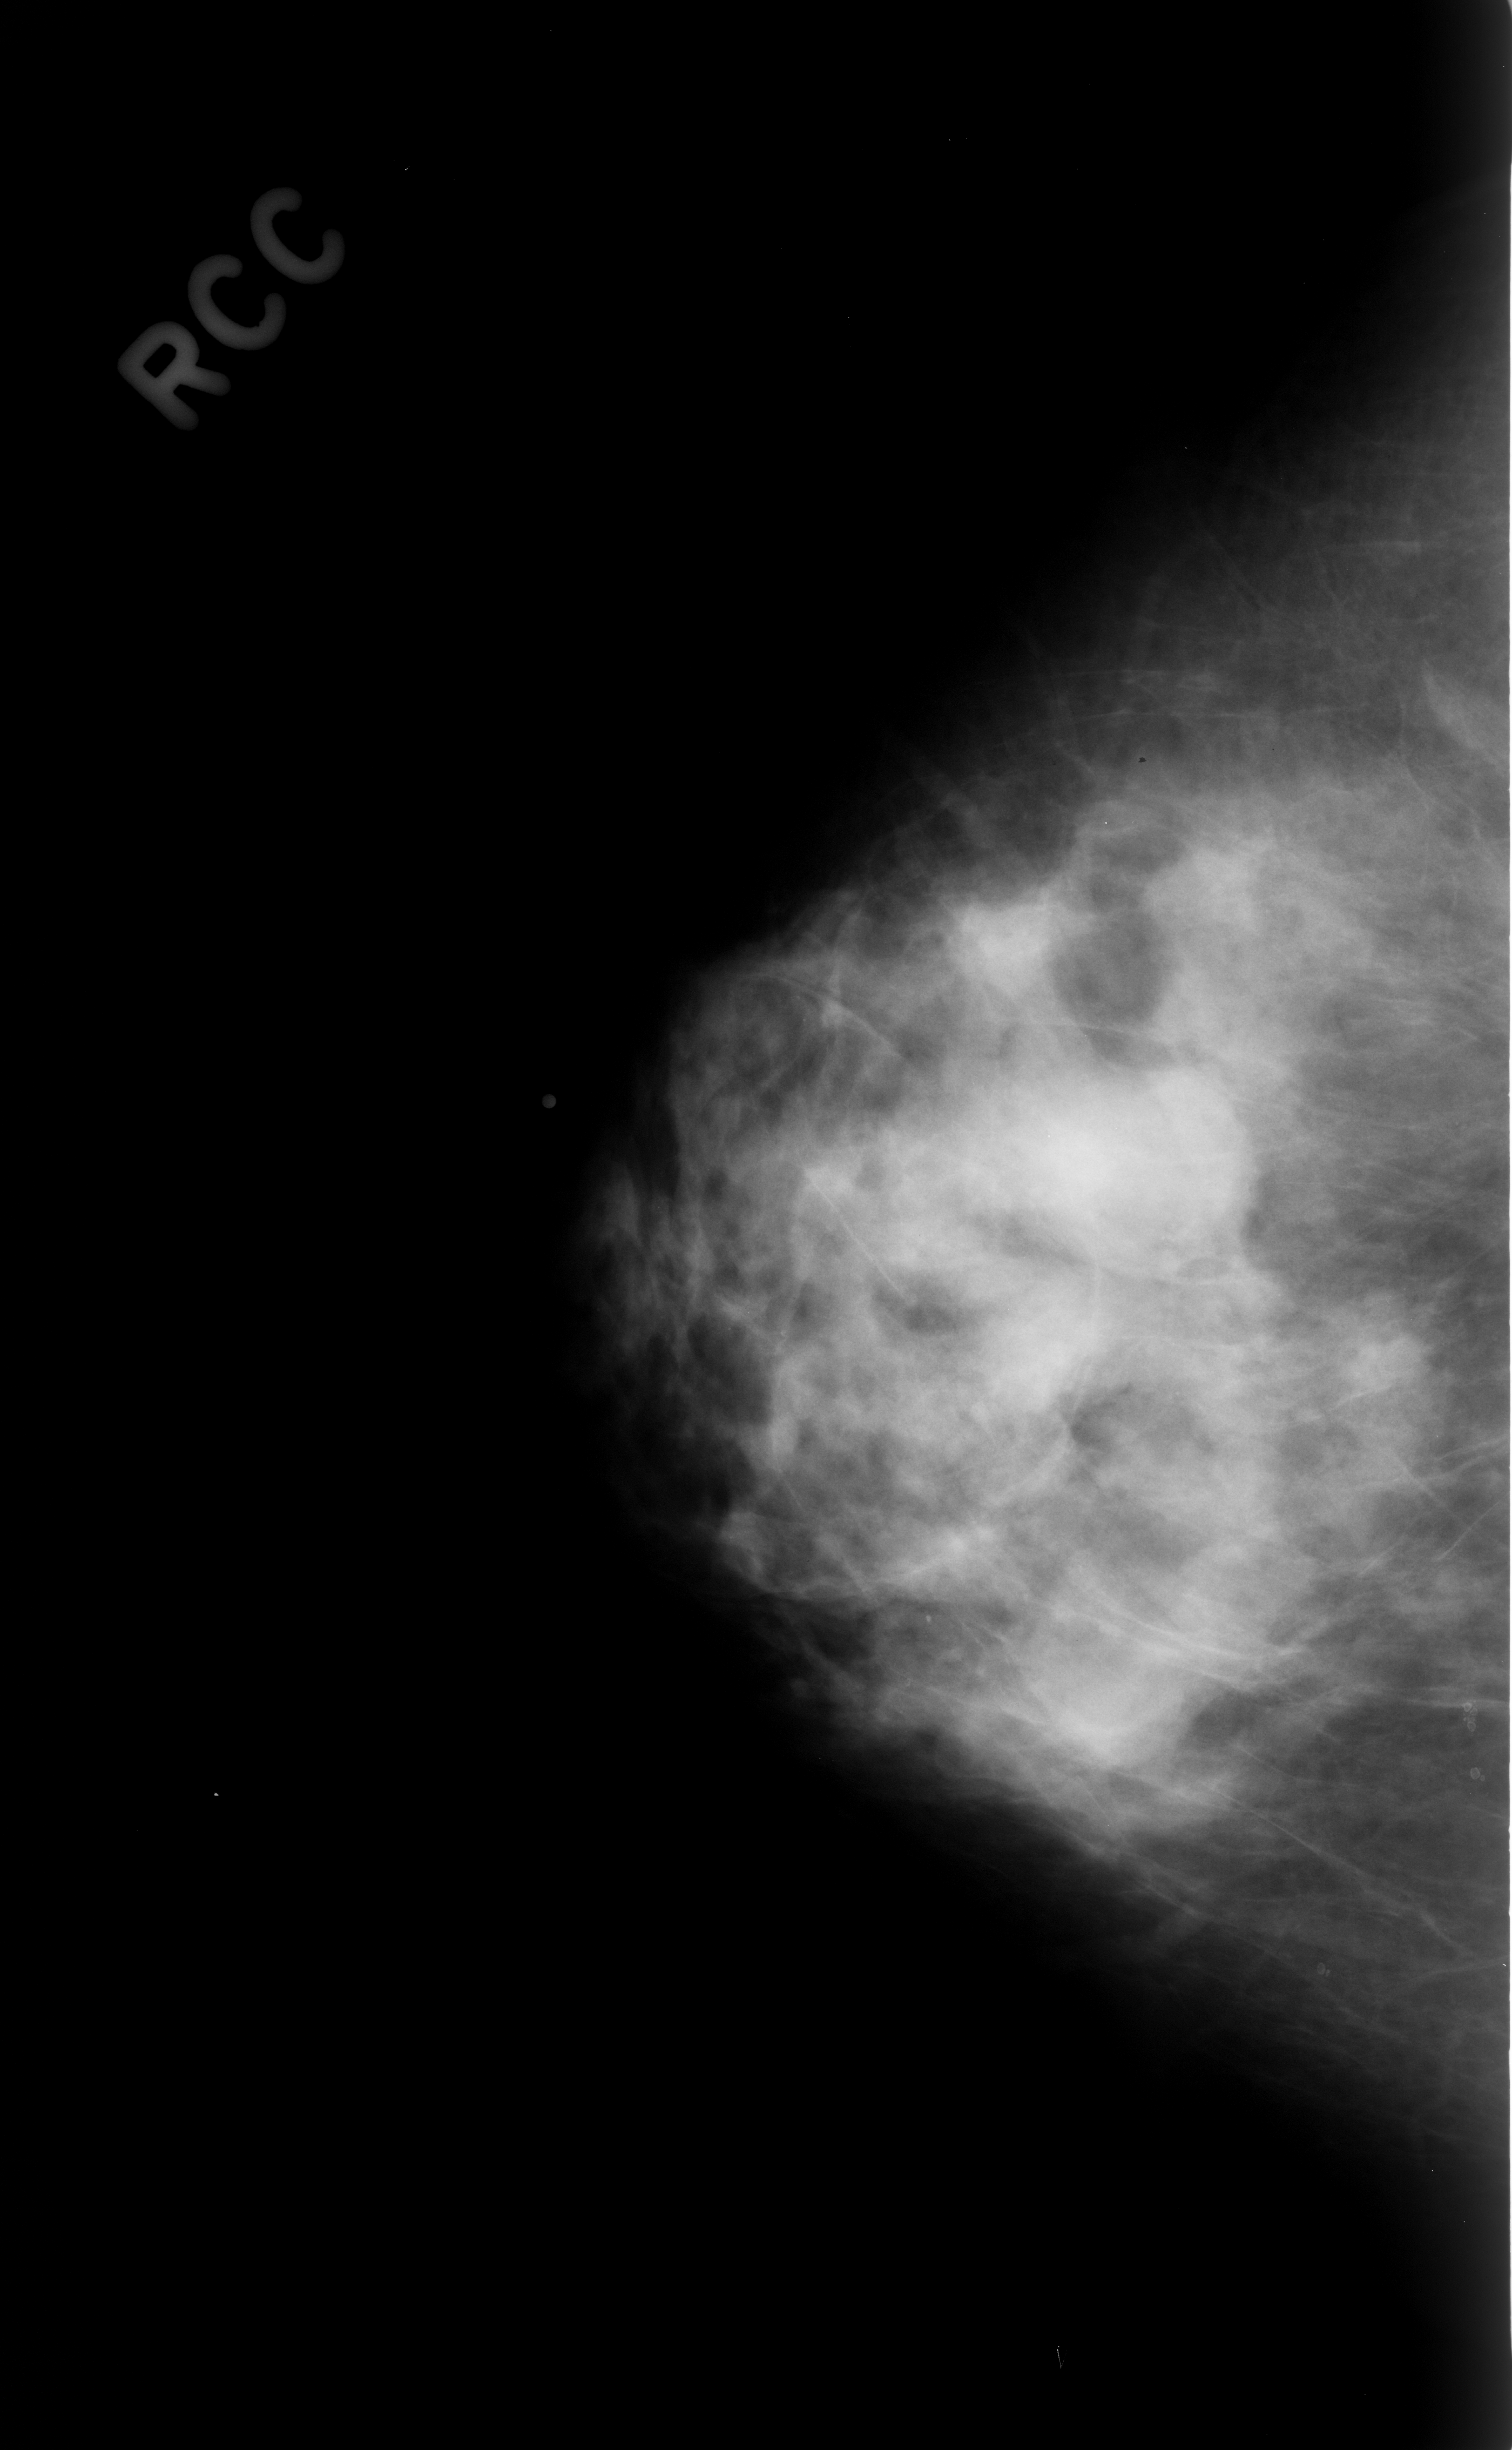
Mammogram (digitized film), right breast, CC view, BI-RADS breast density category 3 (scale 1–4).
Abnormality record for this image: mass, shape oval, margins obscured; BI-RADS assessment category 3; benign without callback (not worked up further).